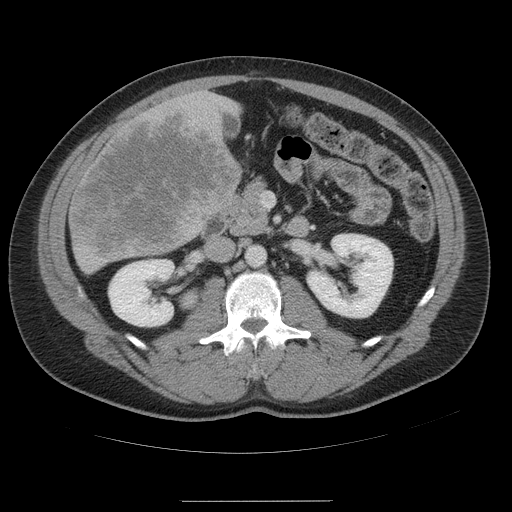
Contrast-enhanced abdominal CT, one axial slice; intravenous contrast given; soft-tissue window (W 400 / L 40 HU); 5 mm slice thickness; 512 × 512 image matrix. Male patient, age 40 years. Case-level facts recorded for this patient, not image findings: diagnosis: colorectal cancer liver metastases, imaged before liver resection; multiple liver metastases: no; largest metastasis: 15 cm.
Annotated regions visible in this slice (manually delineated by an expert):
- liver: box from (x=70, y=92) to (x=242, y=273) px
- liver metastasis: (x=69, y=109)–(x=239, y=260)